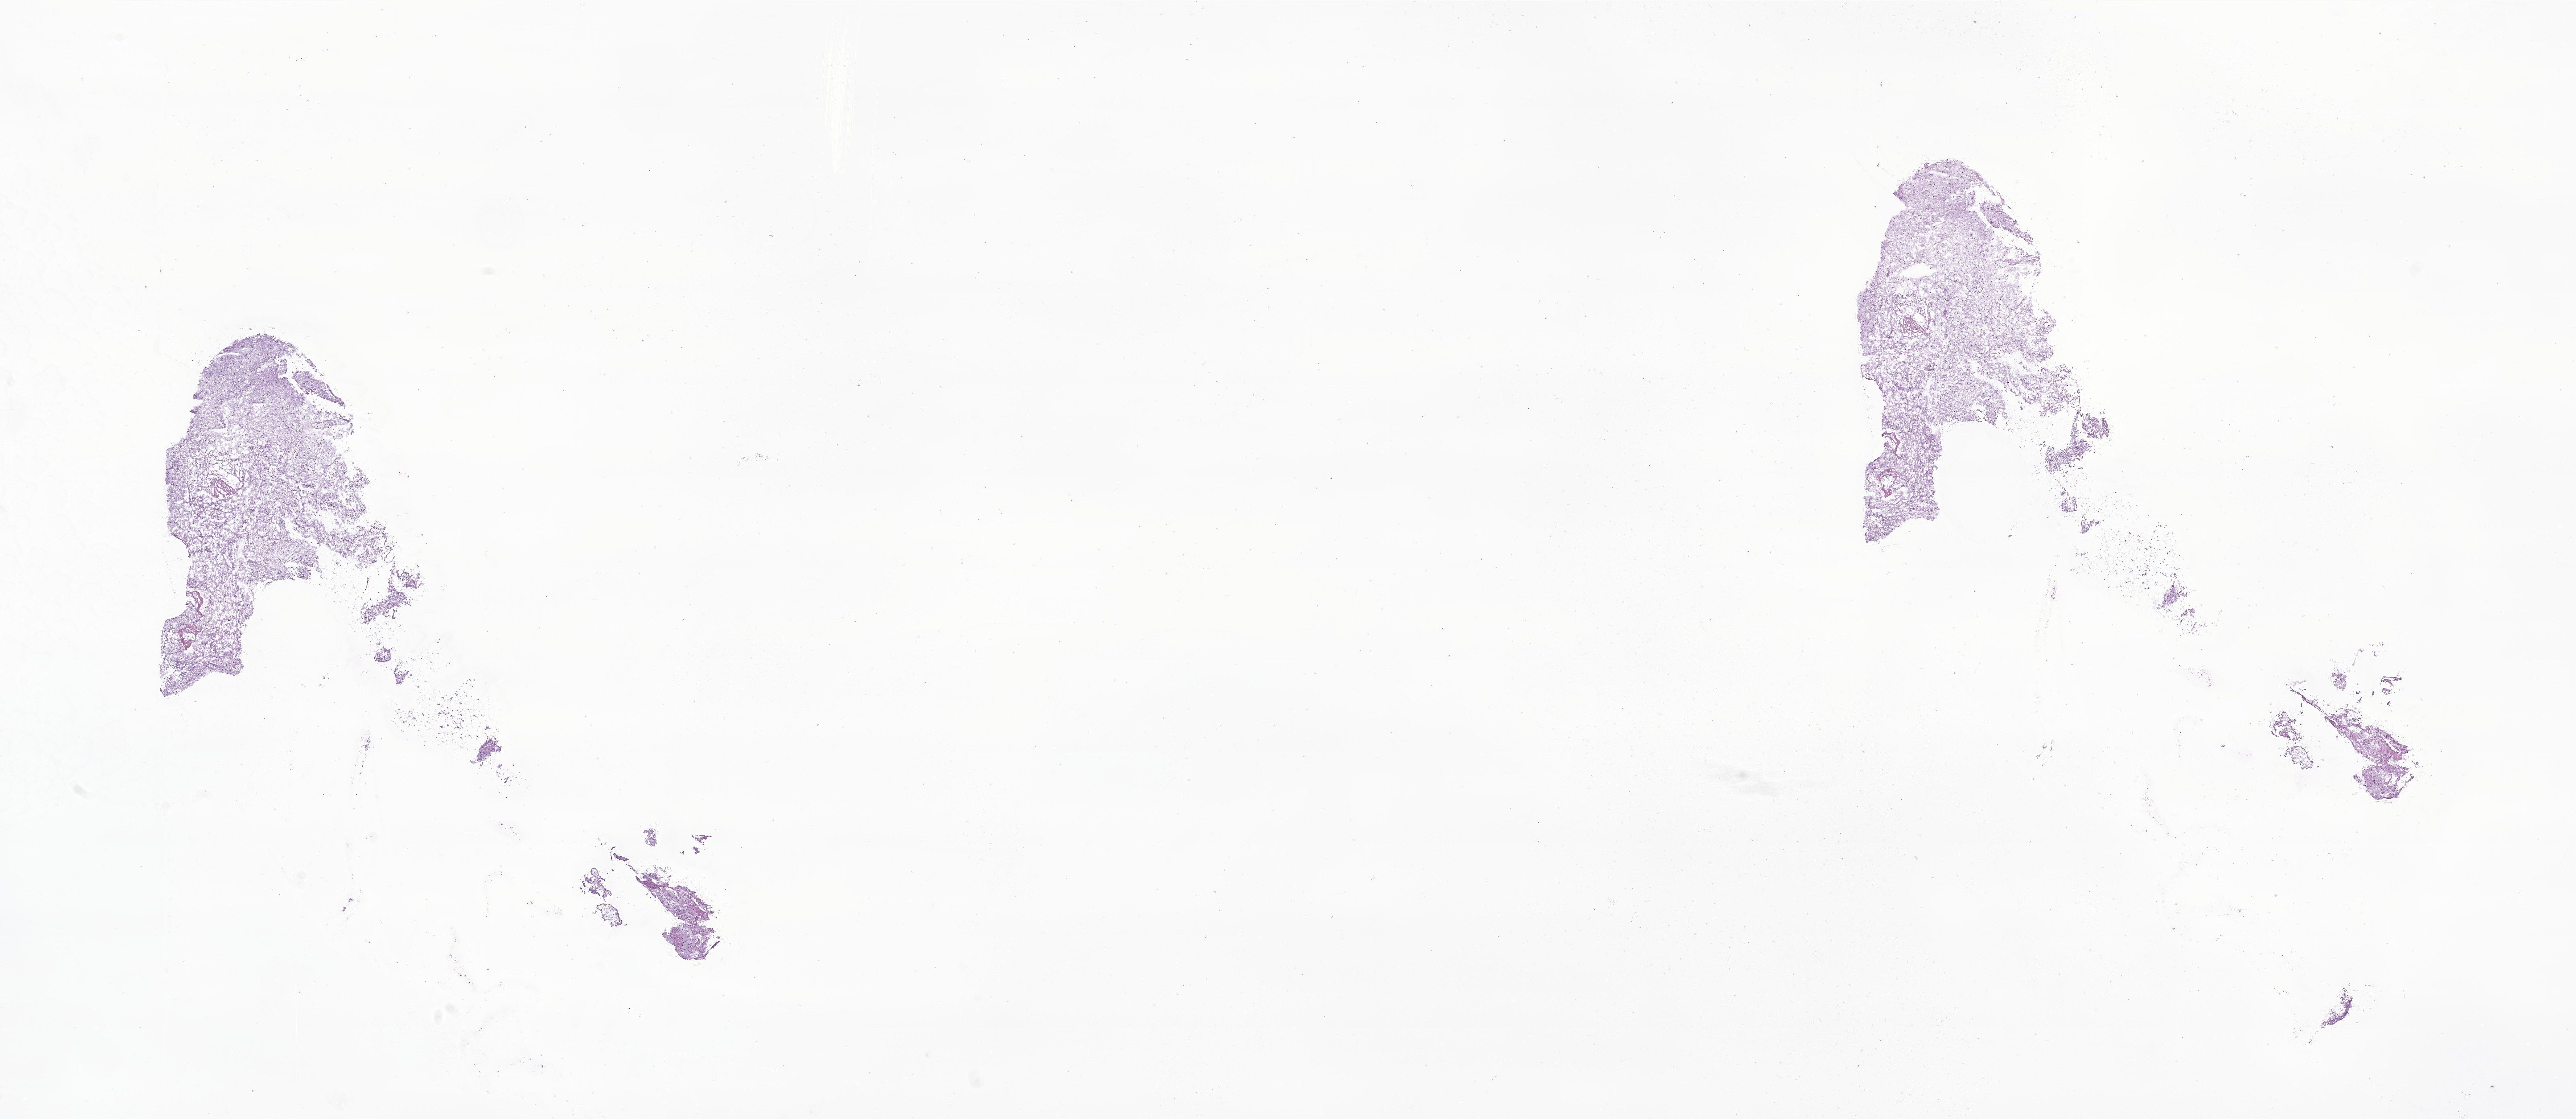
Digitized haematoxylin and eosin-stained section of tumor tissue from the brain — low-resolution overview of the scanned area, about 29.9 x 13.0 mm. Frozen section (OCT-embedded). Patient: female, age 164 months (13 years 8 months).
Recorded diagnosis: Astrocytoma, NOS.